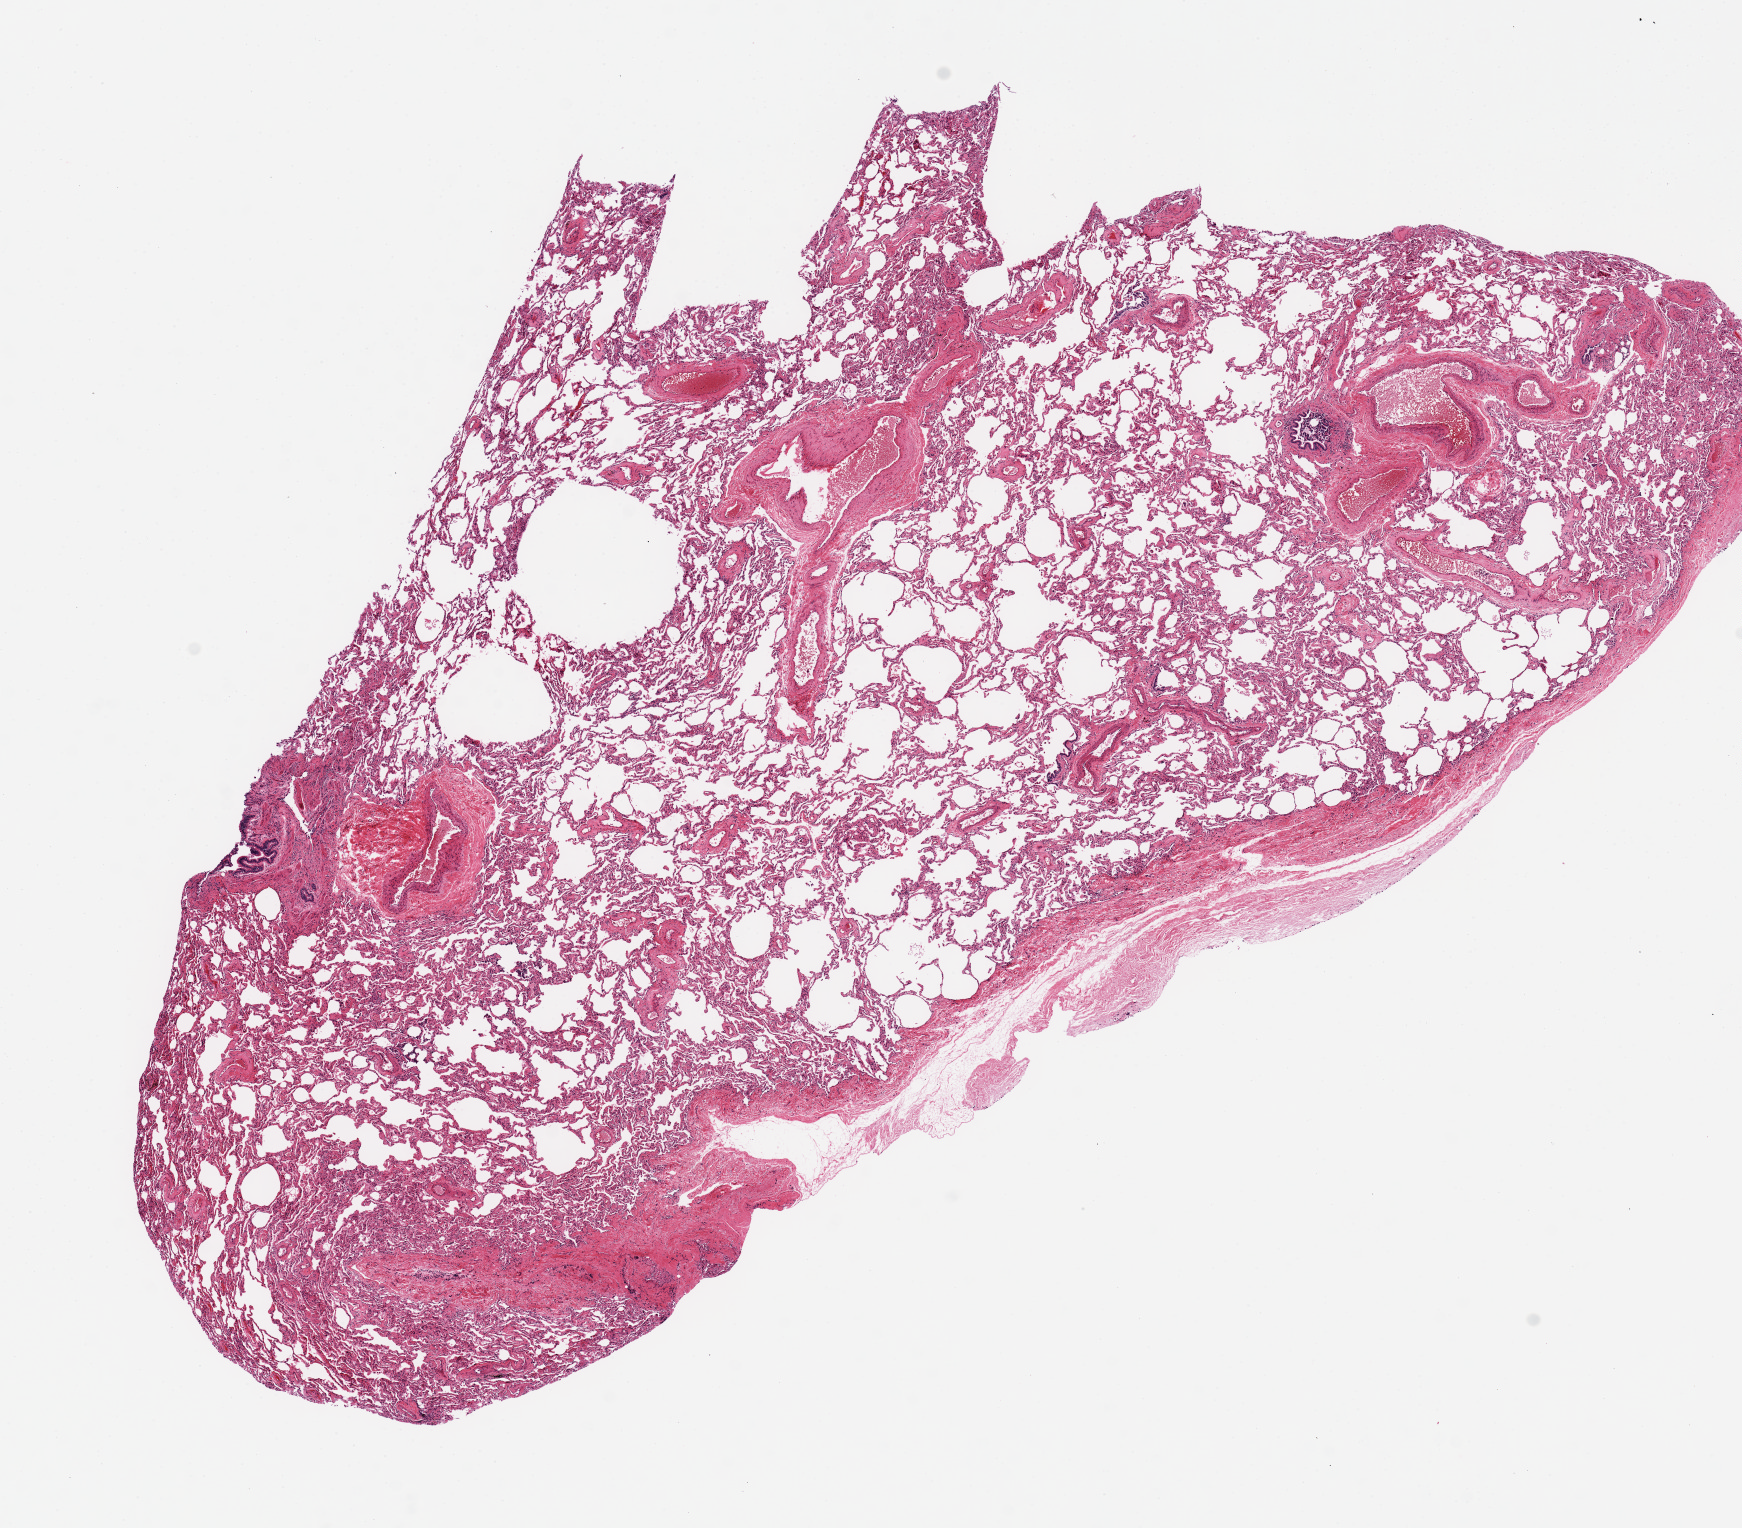
Whole-slide image, haematoxylin and eosin stain — shown as a low-resolution overview of the whole scanned area (about 13.8 x 12.1 mm). PAXgene-fixed paraffin-embedded (PFPE) section. Target tissue: lung. Donor tissue sample.
Pathologist's review note for this sample: Remarkably well-preserved; minimal inflammation.